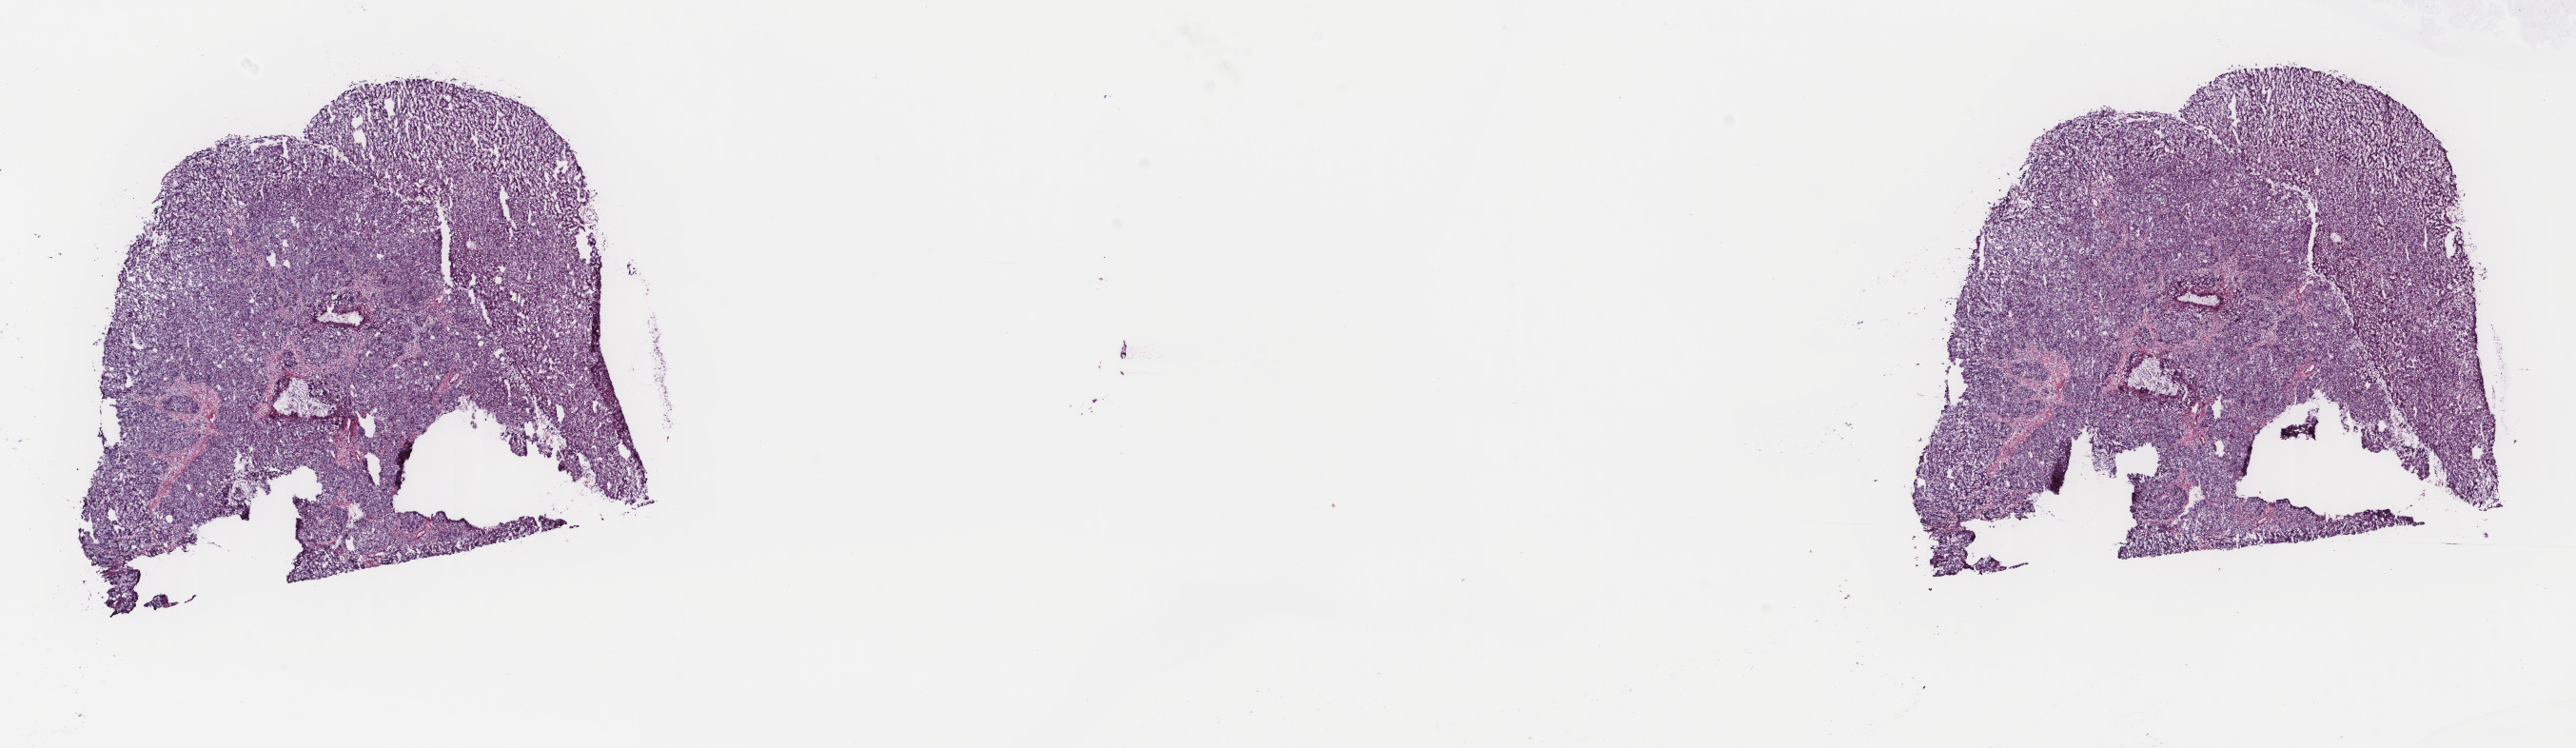
H&E whole-slide image — shown as a low-resolution overview of the whole scanned area (about 21.5 x 6.2 mm, acquisition: 40x scan); frozen section; sample: primary tumour, liver. Male, age 68 years at initial diagnosis. Histologic grade: G2 (moderately differentiated). Composition of this section per pathologist review: tumour cells 100%, tumour nuclei 90%, normal cells 0%, stromal cells 0%, necrosis 0%. Inflammatory infiltration, as recorded: lymphocyte infiltration 0%, monocyte infiltration 0%, neutrophil infiltration 0%.
- TNM: T1 N0 M0
- AJCC pathologic stage: I (7th edition)
- diagnosis: Hepatocellular carcinoma, NOS